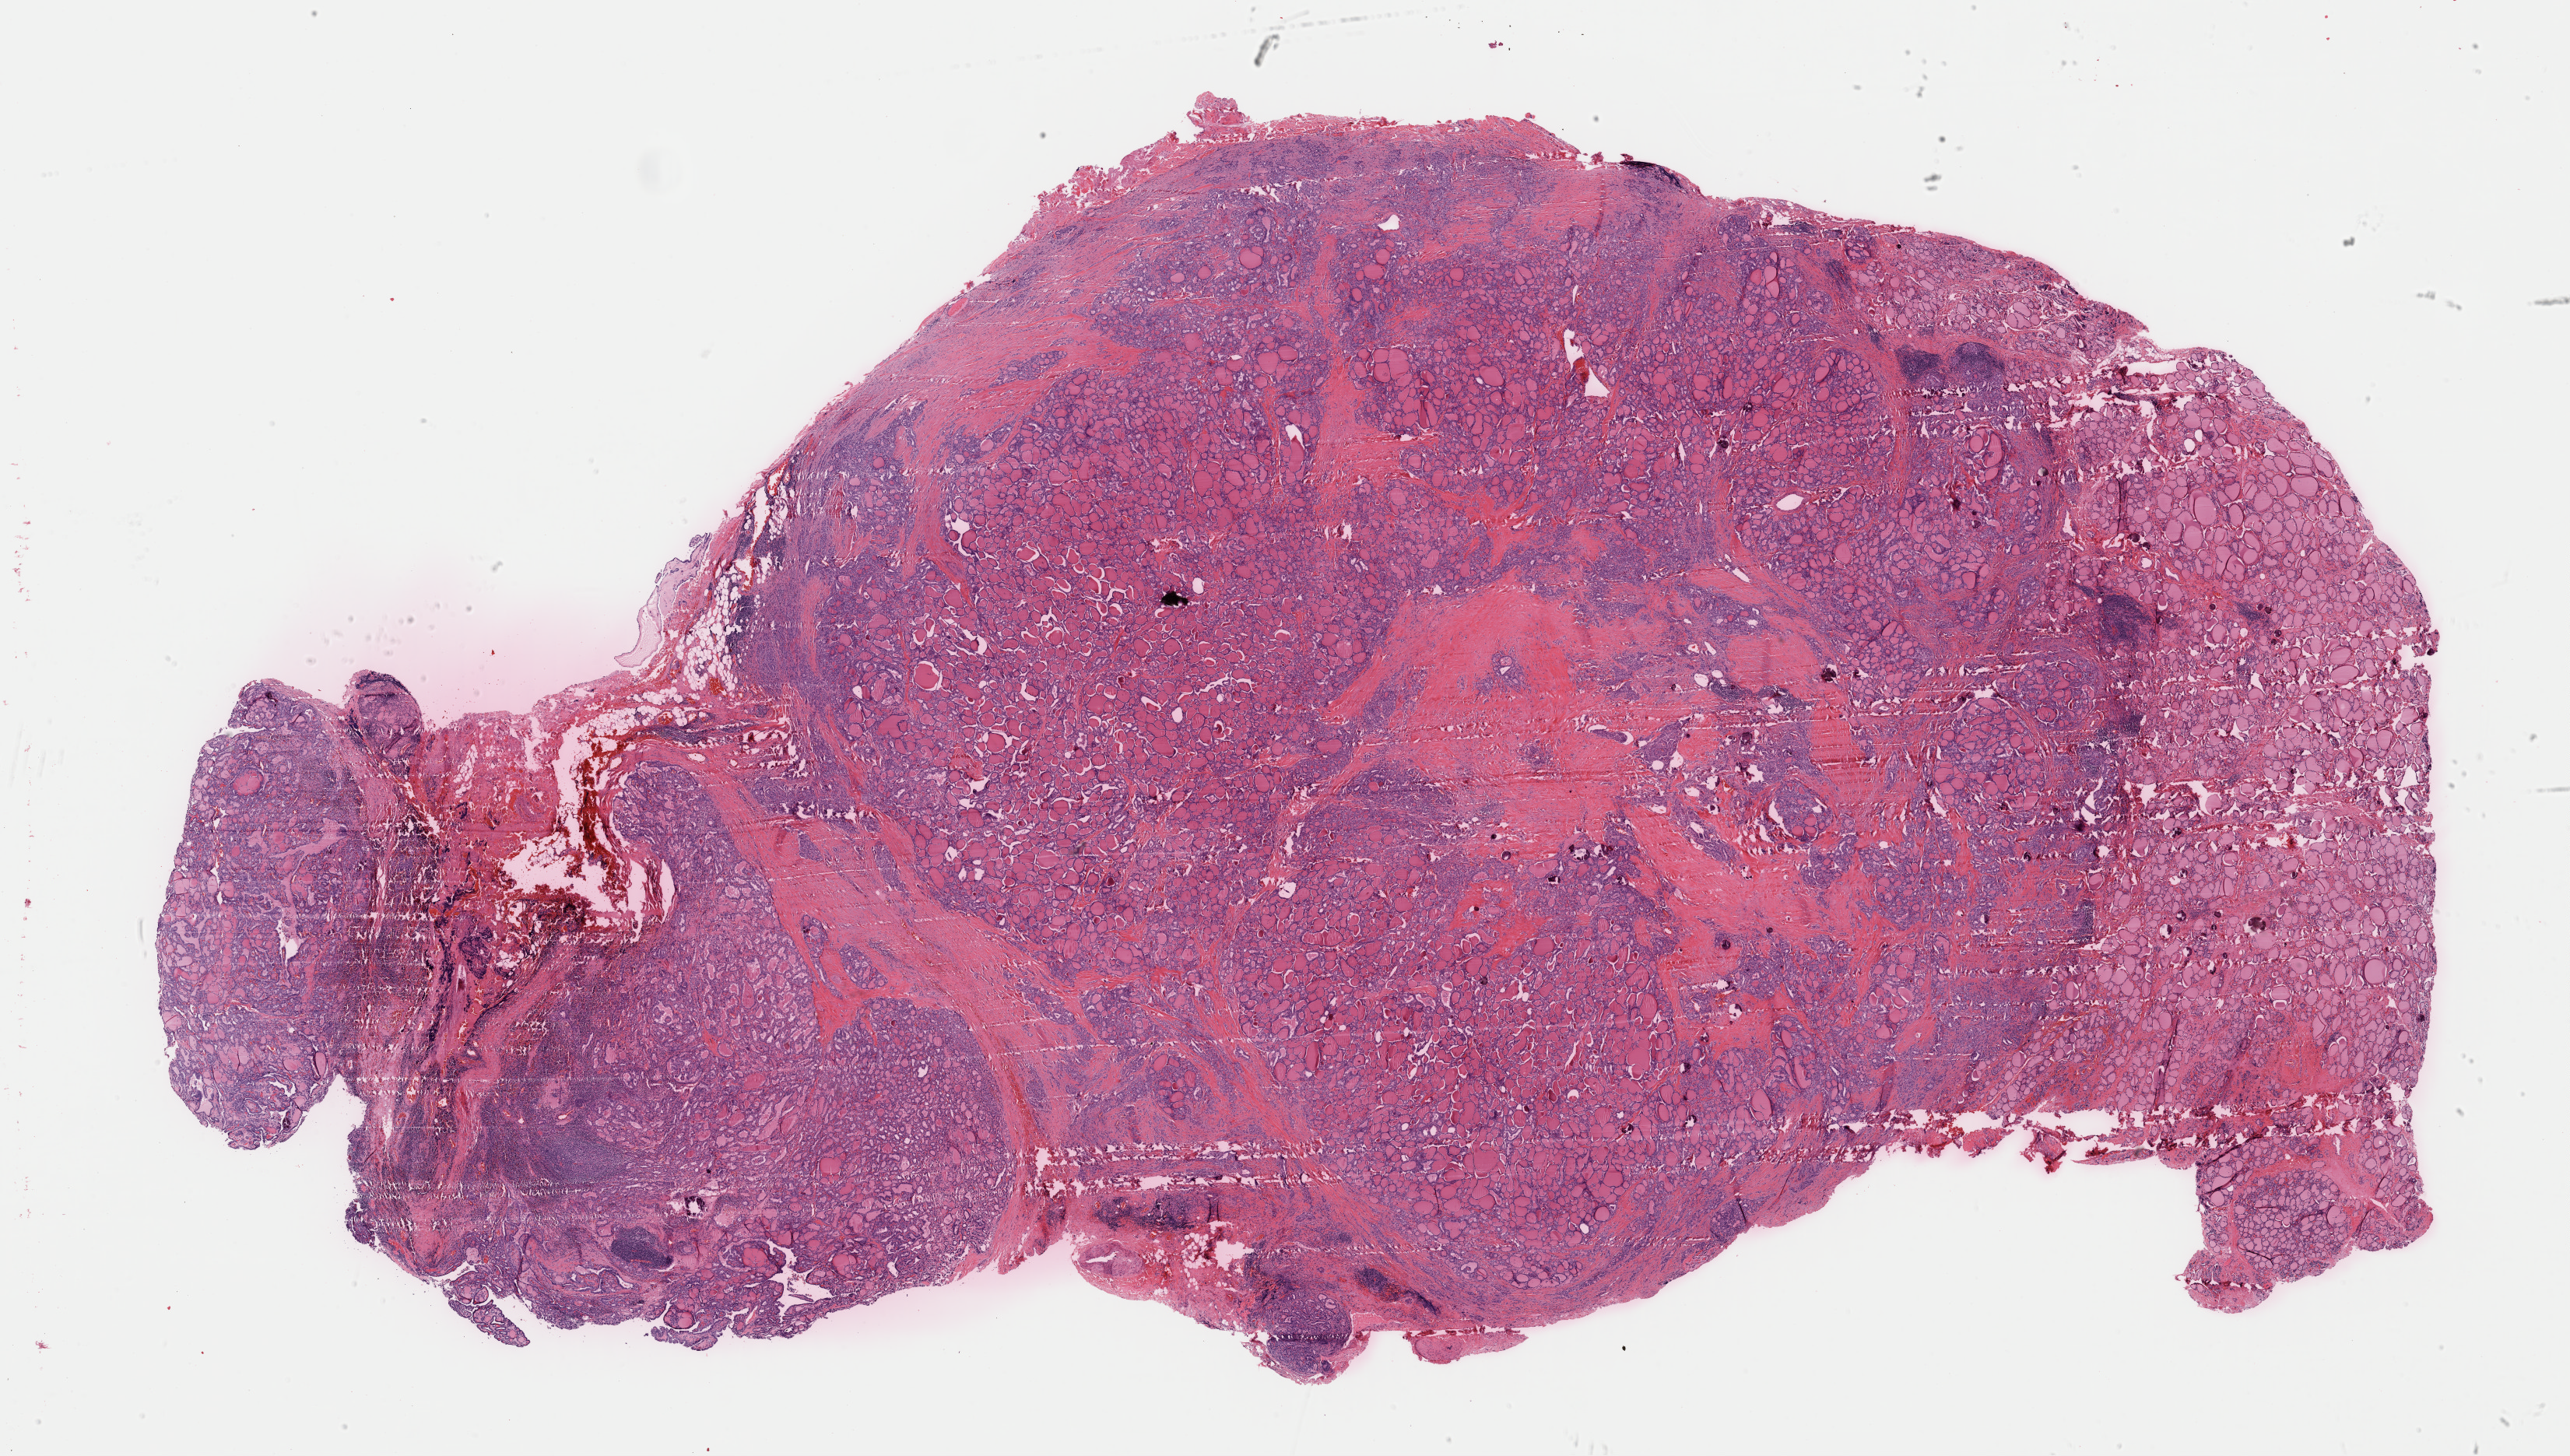
Hematoxylin and eosin (H&E) stained whole-slide image, whole scanned area (about 26.1 x 14.8 mm, from a 40x scan) shown as a low-resolution overview, FFPE section, sample: primary tumour, thyroid. Female, age 47 years at initial diagnosis.
Lymph nodes positive (case pathology): 7 of 20 examined. Laterality: right. Diagnosis: Papillary adenocarcinoma, NOS (thyroid gland). TNM: T3 N1a M0. AJCC pathologic stage: III.